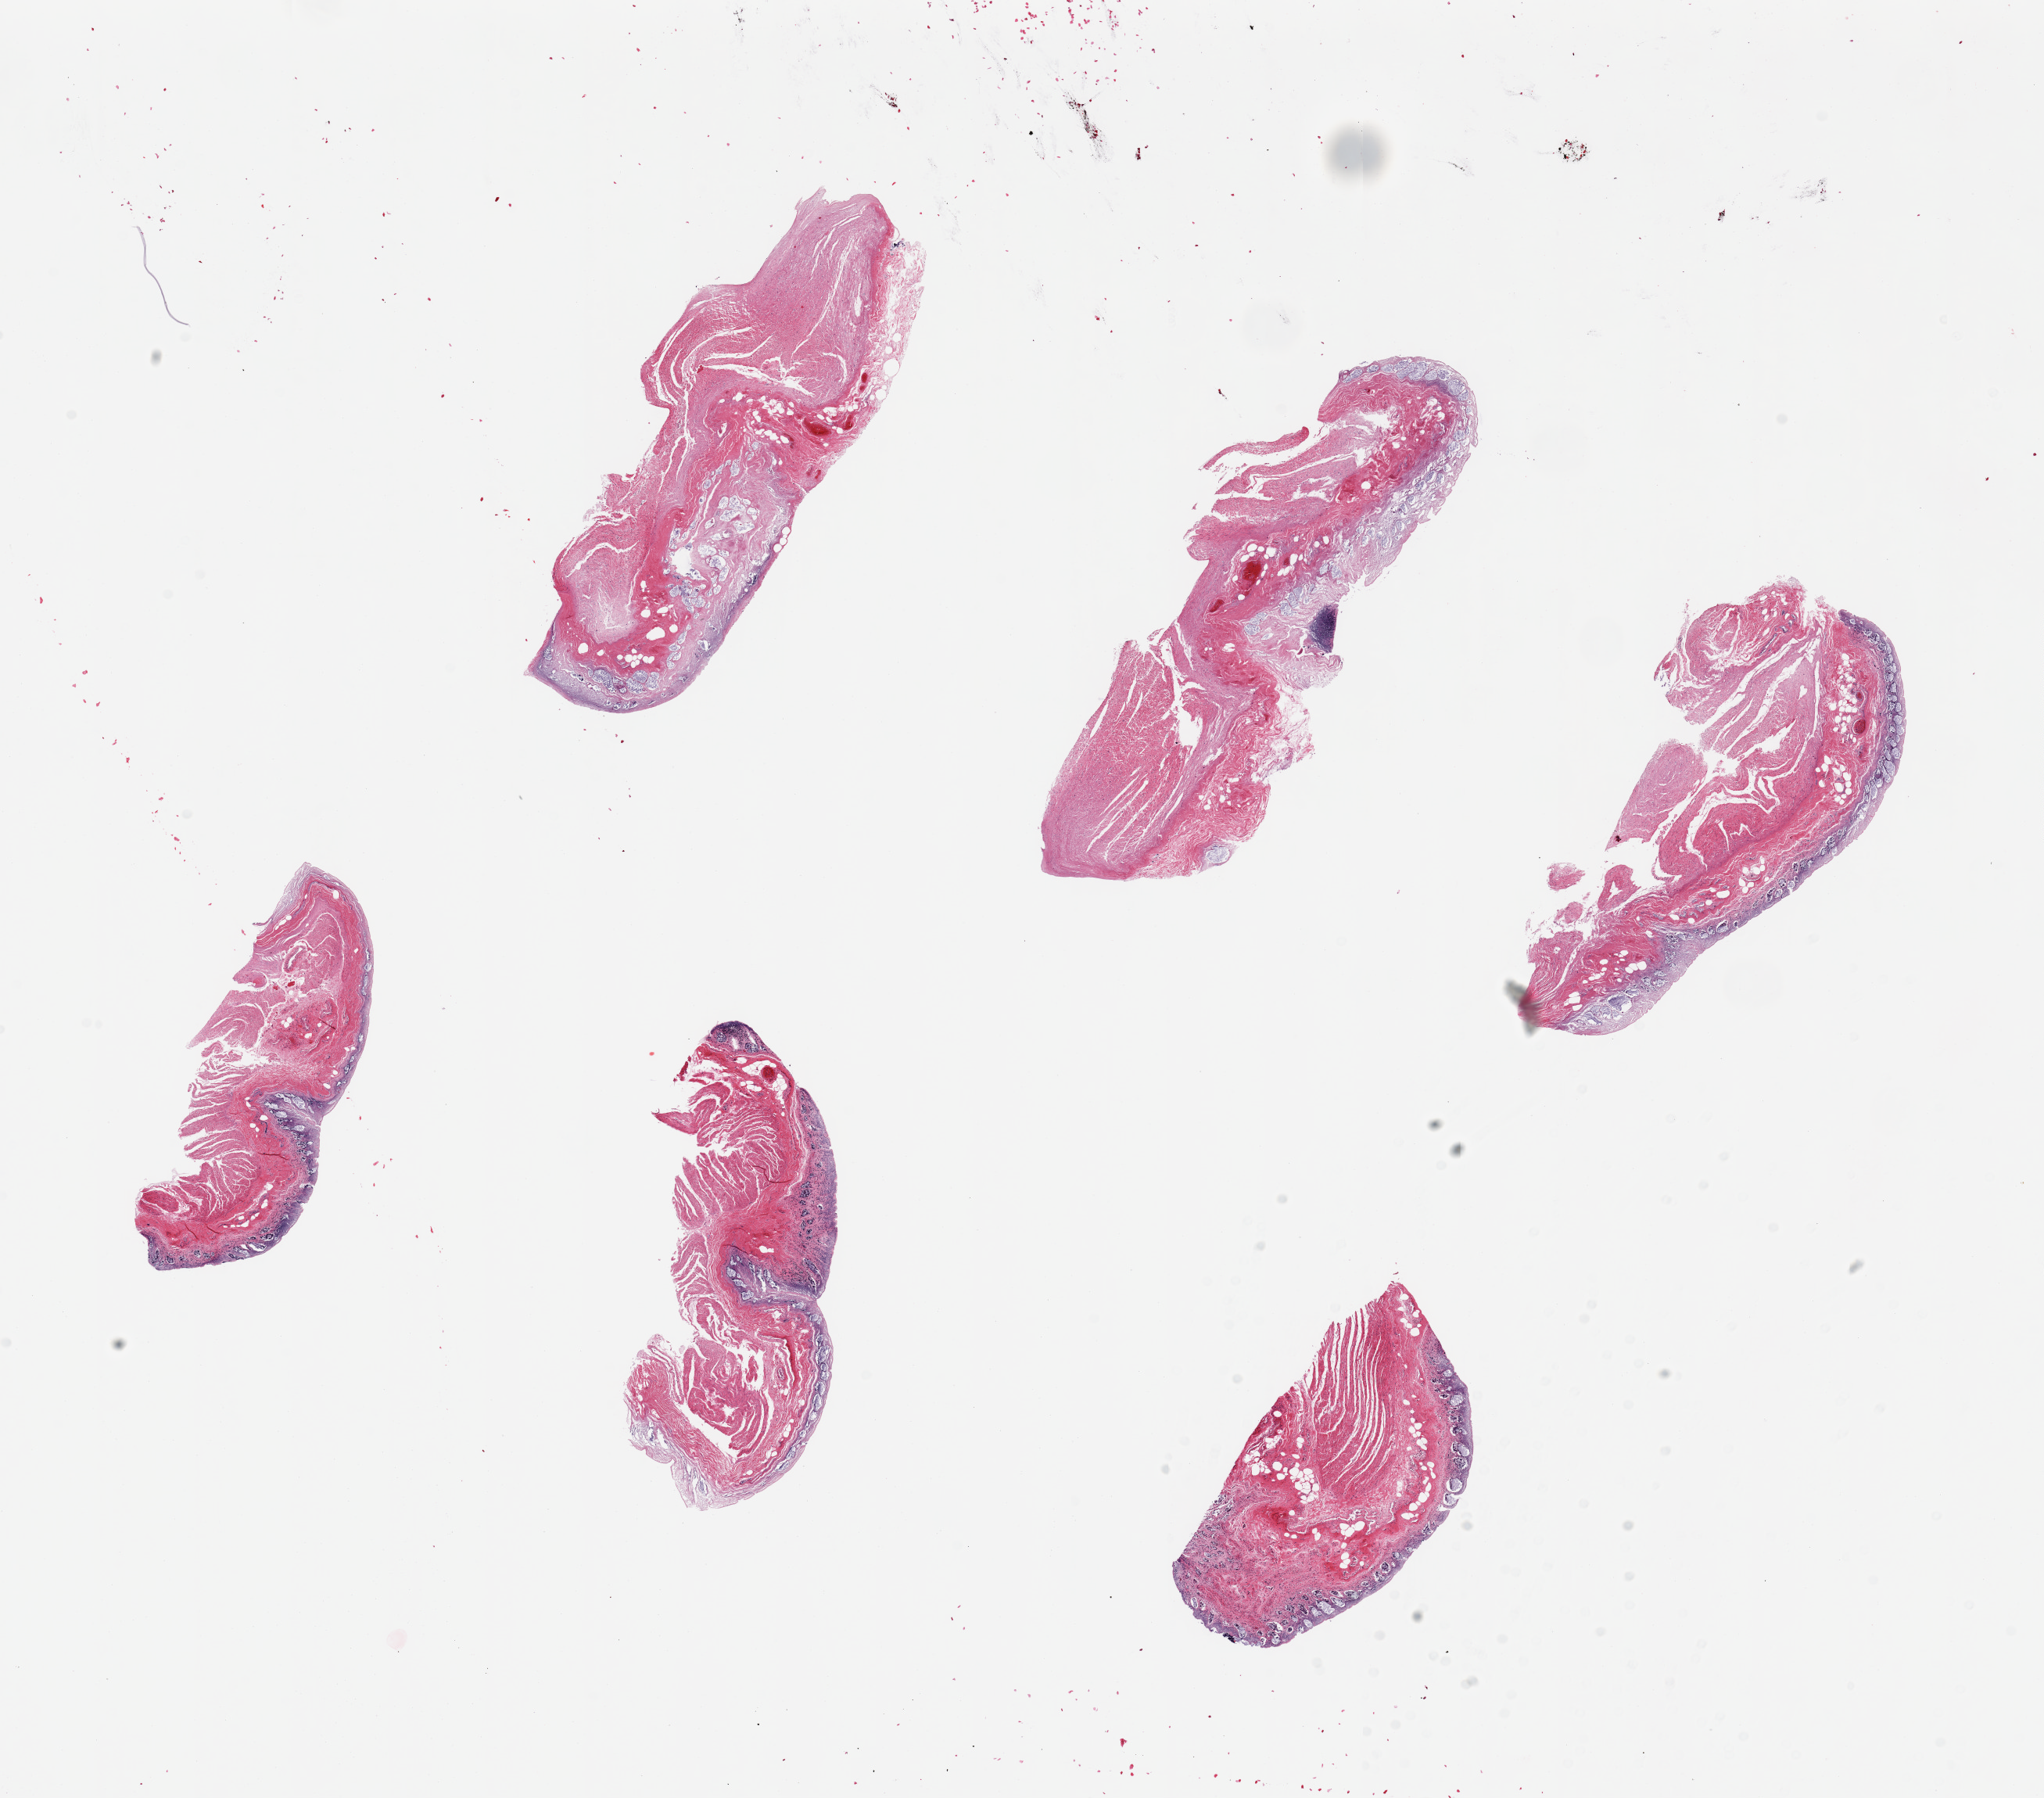
Whole-slide image, hematoxylin and eosin (H&E) stain, whole scanned area (about 20.7 x 18.2 mm) shown as a low-resolution overview; PAXgene-fixed, paraffin-embedded tissue; sampled site (target tissue): sigmoid colon; tissue donor sample. Male donor.
Reviewer comment on this tissue sample: 6 pieces, up to 6.5x2mm; mucosa (unwanted) and muscle (target) in all pieces.